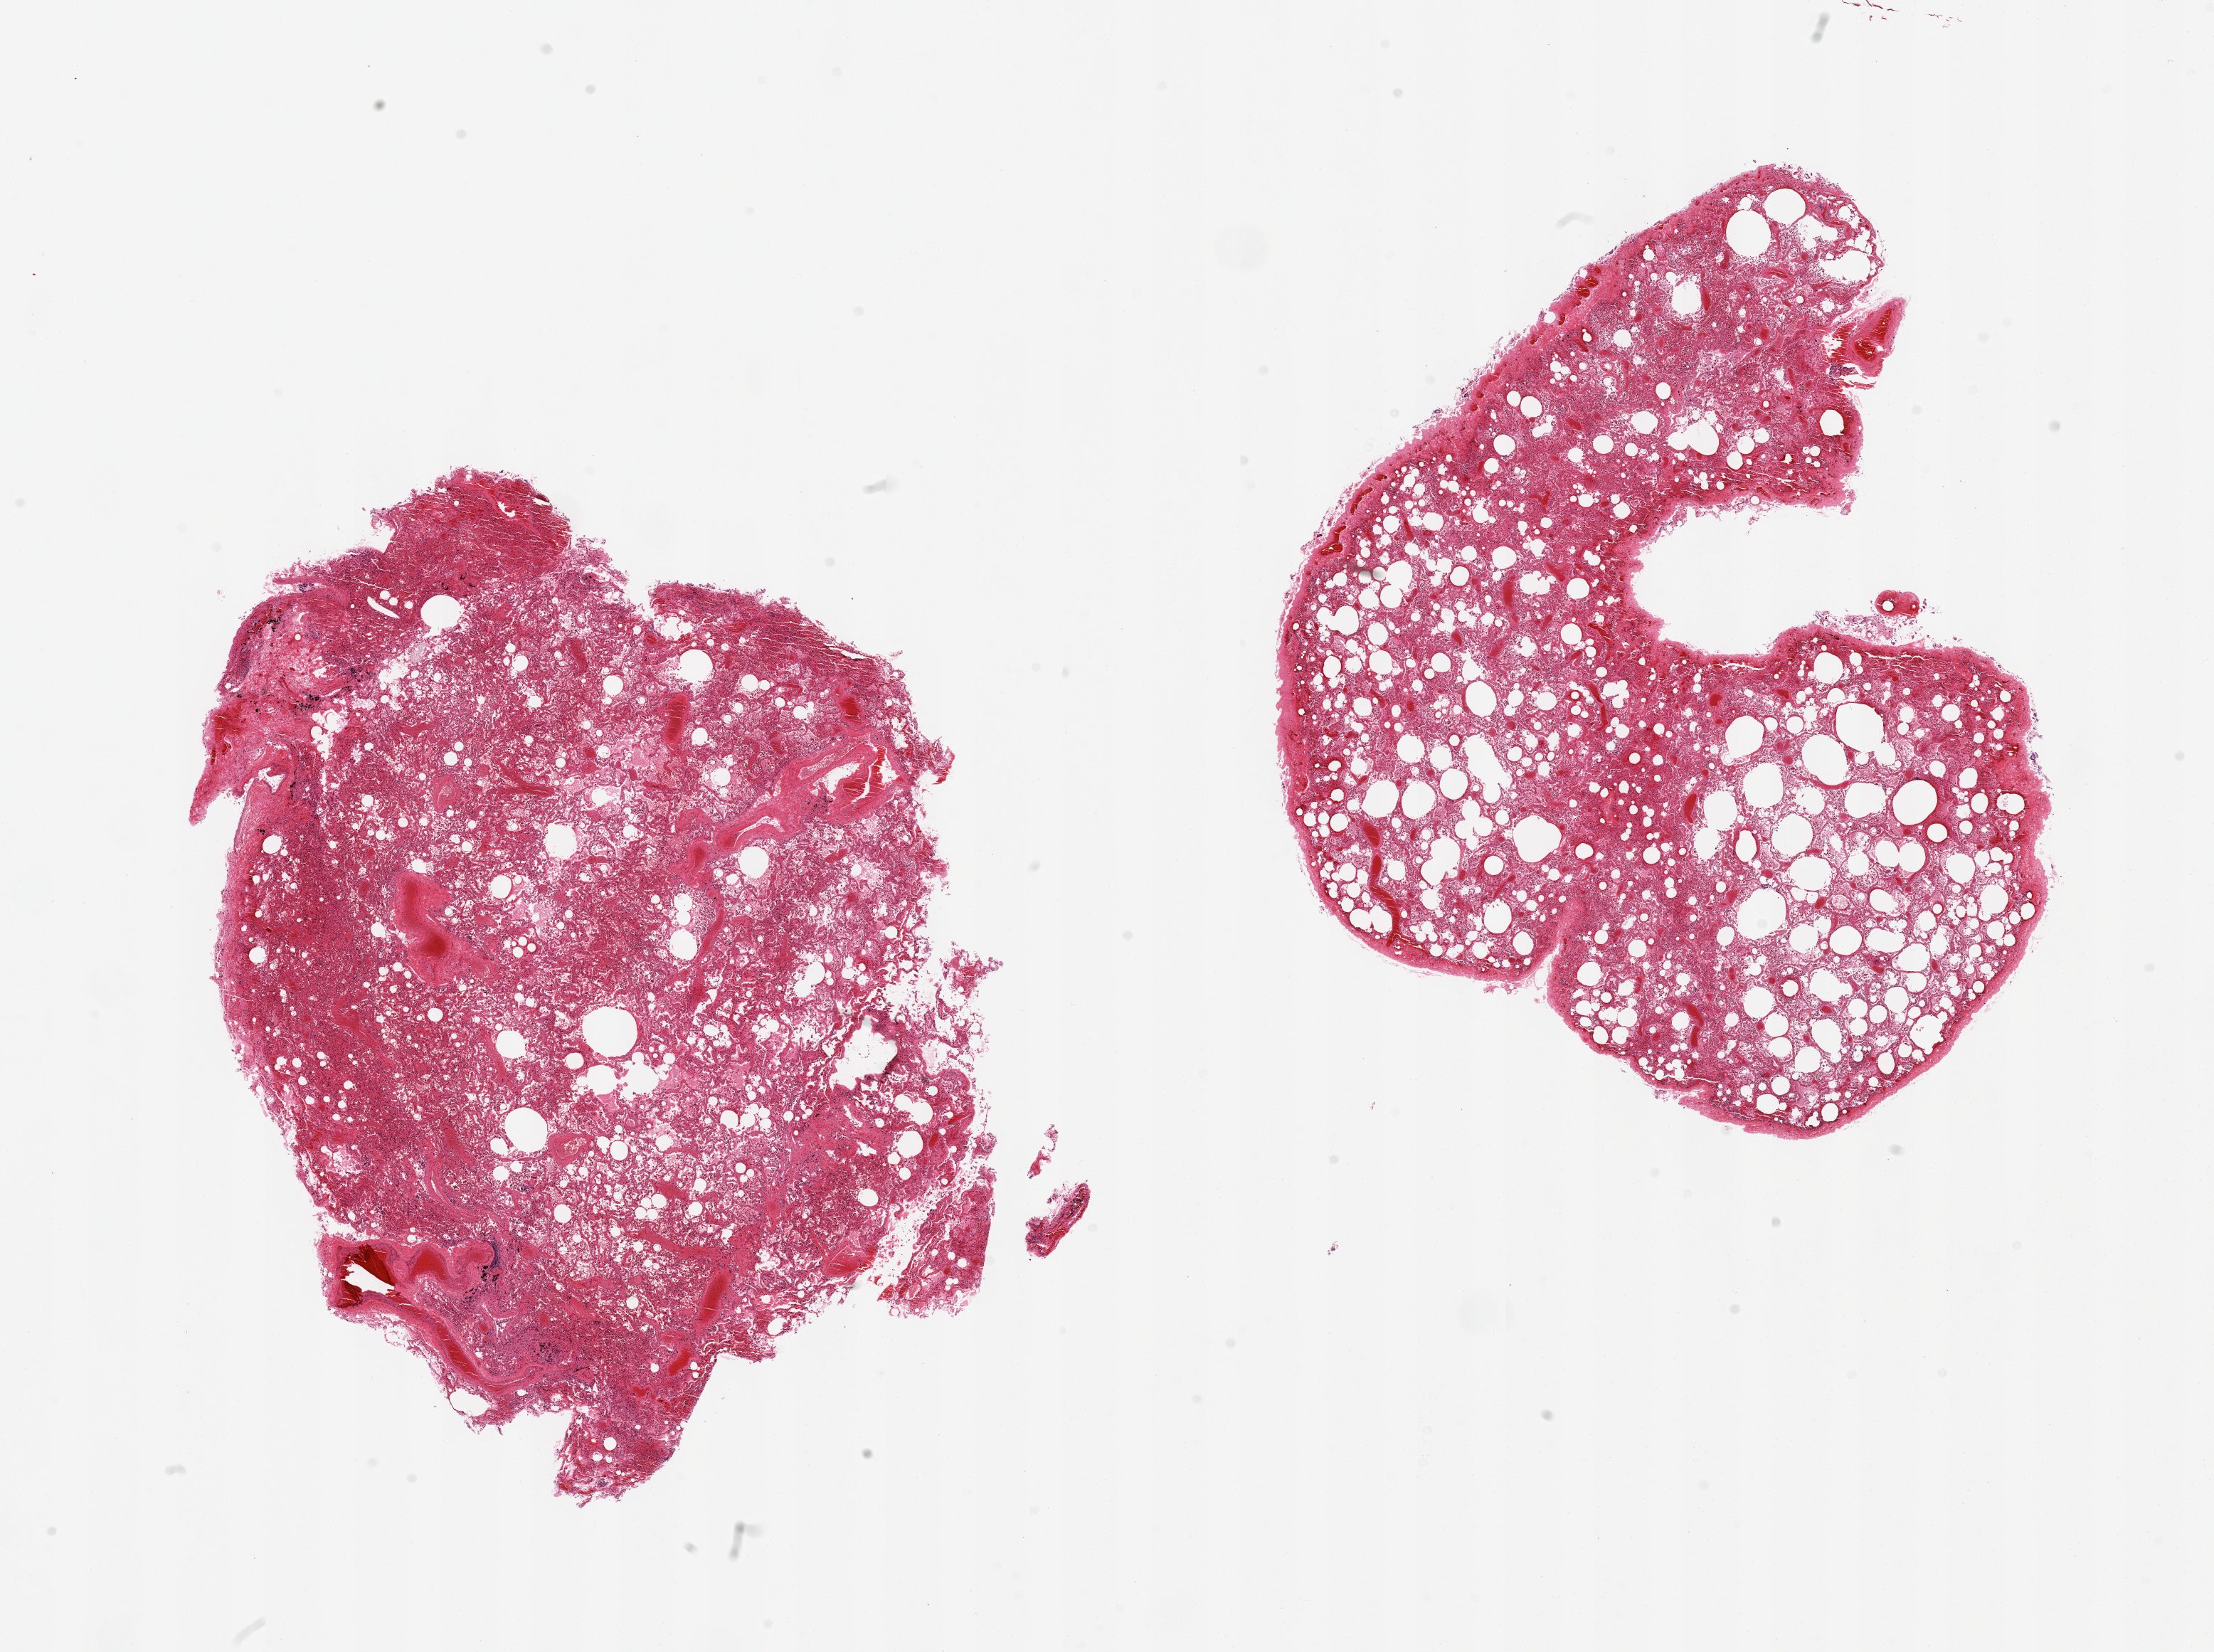
Hematoxylin and eosin (H&E) whole-slide image, brightfield, a low-resolution overview of the entire scanned area, about 24.6 x 18.4 mm, PAXgene-fixed, paraffin-embedded tissue, sampled site (target tissue): lung, tissue donor sample.
* pathologist's review note for this sample: 2 pieces; moderate vascular congestion